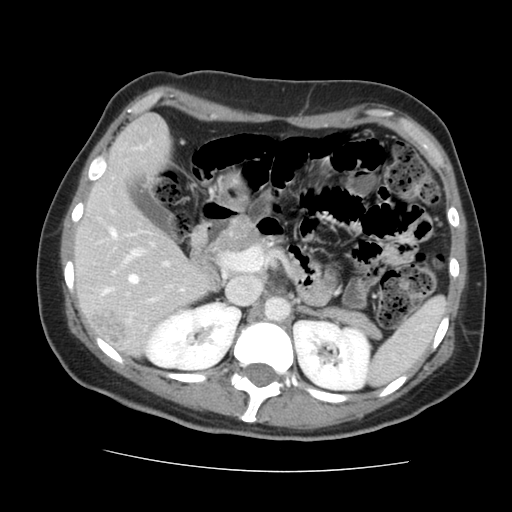
Contrast-enhanced abdominal CT, one axial slice. Slice 85 of 144 in the series (ordered by position). 120 kVp. Intravenous contrast given. Soft-tissue window (W 400 / L 40 HU). 2.5 mm slice thickness. 512 × 512 image matrix, field of view 333 × 333 mm. Female patient, age 46 years. Case-level facts recorded for this patient, not image findings: diagnosis: colorectal cancer liver metastases, imaged before liver resection; multiple liver metastases: no; largest metastasis: 2.8 cm; disease in both lobes: no.
Outlined on this slice (manually delineated by an expert):
- hepatic veins: box from (x=102, y=274) to (x=139, y=295) px
- liver: (x=77, y=116)–(x=210, y=352)
- planned liver remnant (the part of the liver to remain after resection): (x=77, y=116)–(x=210, y=348)
- portal vein (with intrahepatic branches): (x=111, y=230)–(x=226, y=302)
- liver metastasis: (x=92, y=309)–(x=126, y=342)